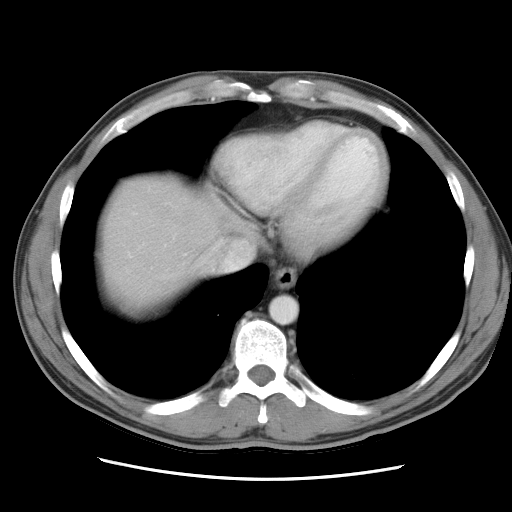
Contrast-enhanced abdominal CT, one axial slice. Position 27 of 34 along the scan axis. Reconstruction kernel STANDARD. Intravenous contrast given. Soft-tissue window (W 400 / L 40 HU). 512 × 512 image matrix, field of view 360 × 360 mm. Male patient, age 40 years. From the clinical record (not read from this slice): diagnosis: colorectal cancer liver metastases, imaged before liver resection; multiple liver metastases: yes; largest metastasis: 1.5 cm; chemotherapy before resection: no.
Outlined on this slice (expert manual segmentation):
- hepatic veins: box from (x=163, y=256) to (x=249, y=277) px
- liver: (x=99, y=177)–(x=254, y=310)
- planned liver remnant (the part of the liver to remain after resection): (x=99, y=177)–(x=255, y=312)